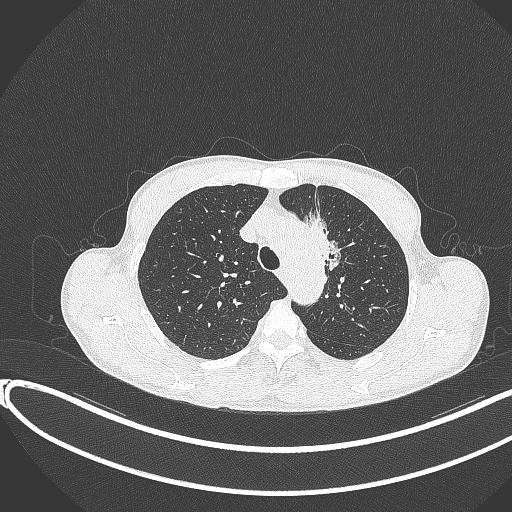
Chest CT, one axial slice; slice 291 of 374 in the series (ordered by position); 120 kVp; lung window (W 1500 / L -600 HU); 1 mm slice thickness; 512 × 512 image matrix, field of view 400 × 400 mm. Male patient, age 58 years. From the clinical record (not read from this slice): clinical TNM (as recorded): T1c N1 M0.
Outlined on this slice (bounding box drawn by a radiologist):
- lung tumour (recorded histology: adenocarcinoma): bounding box <298,209,339,271> (left, top, right, bottom; pixels)